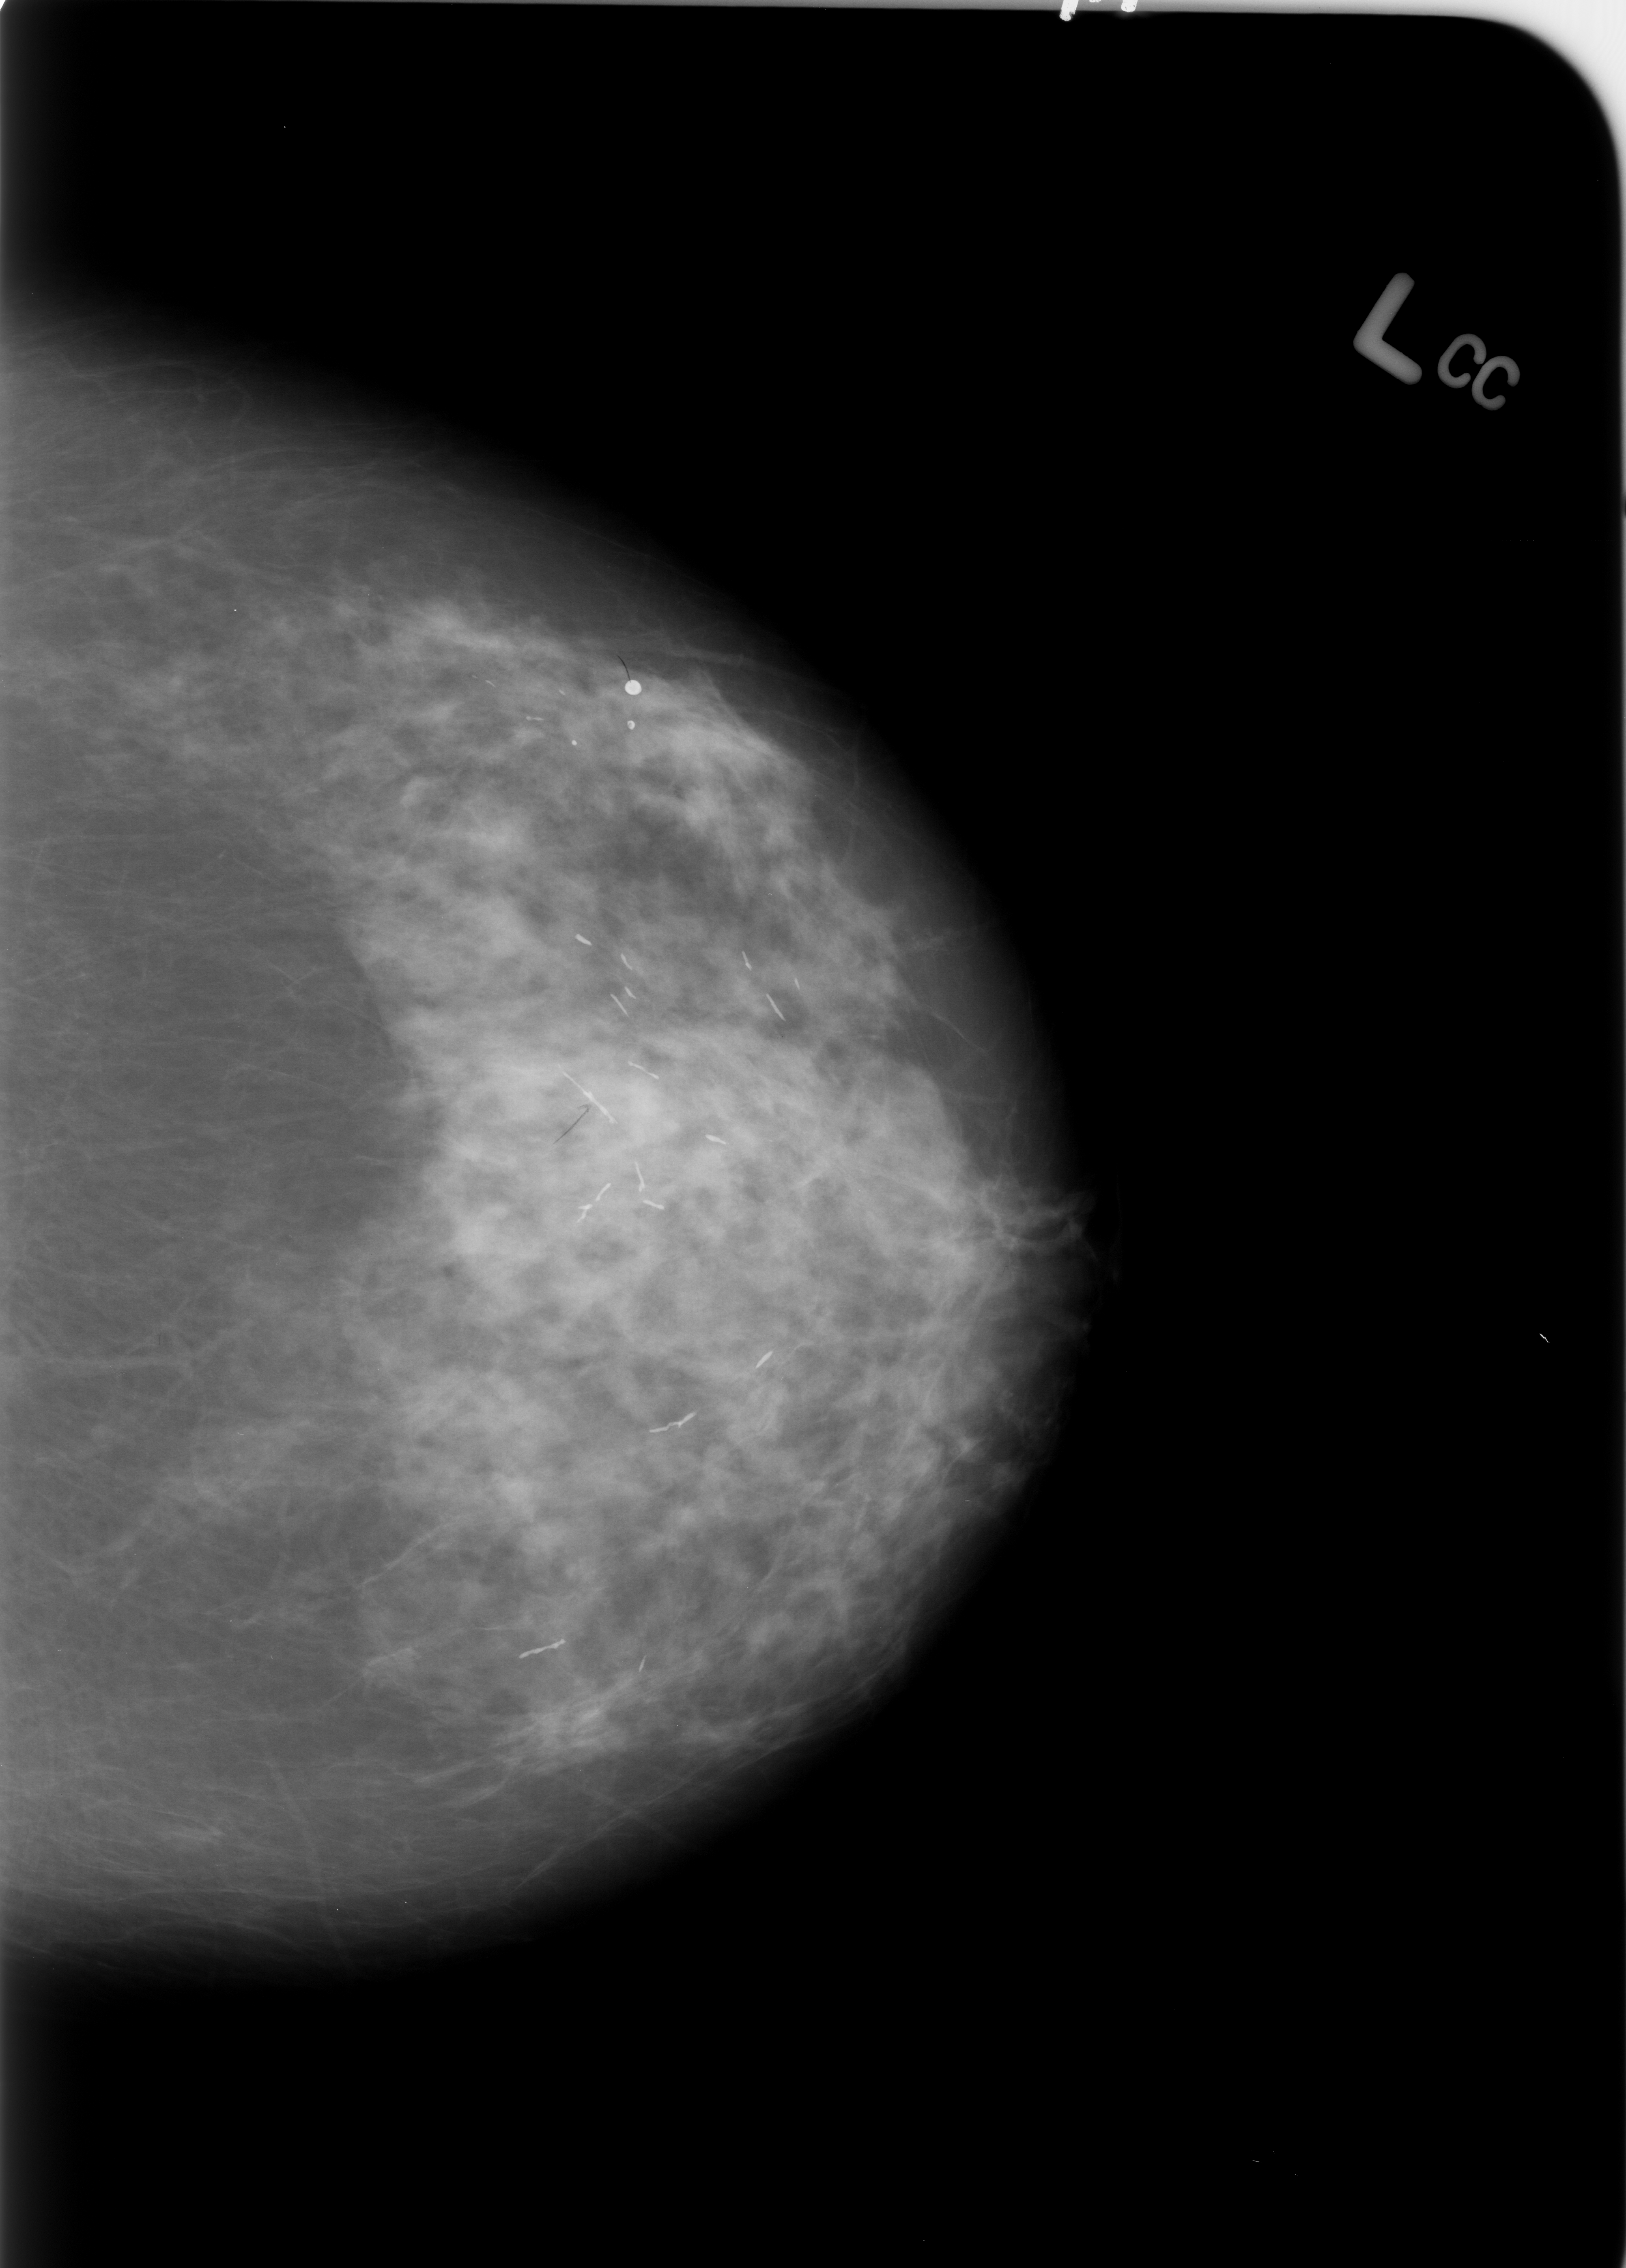
Mammogram (digitized film); left breast; CC view; breast composition: heterogeneously dense (BI-RADS density category 3 of 4); 1626 × 2268 image matrix.
Expert-marked regions of interest on this film, with their recorded descriptors:
- Finding 1 of 6: calcifications, morphology large rodlike / round and regular, distribution regional; BI-RADS assessment category 2; subtlety rating 5 on a 1 (subtle) to 5 (obvious) scale; benign; no additional work-up was recommended (outcome (as recorded, no biopsy): benign without callback): box from (x=499, y=1625) to (x=588, y=1669) px
- Finding 2 of 6: calcifications, morphology large rodlike / round and regular, distribution regional; BI-RADS assessment category 2; subtlety rating 5 on a 1 (subtle) to 5 (obvious) scale; outcome (as recorded, no biopsy): benign without callback (not worked up further): (x=561, y=1077)–(x=673, y=1221)
- Finding 3 of 6: calcifications, morphology large rodlike / round and regular, distribution regional; BI-RADS assessment category 2; subtlety rating 5 on a 1 (subtle) to 5 (obvious) scale; benign; no additional work-up was recommended (outcome (as recorded, no biopsy): benign without callback): (x=564, y=918)–(x=656, y=1036)
- Finding 4 of 6: calcifications, morphology large rodlike / round and regular, distribution regional; BI-RADS assessment category 2; benign; no additional work-up was recommended (outcome (as recorded, no biopsy): benign without callback): (x=606, y=668)–(x=663, y=741)
- Finding 5 of 6: calcifications, morphology large rodlike / round and regular, distribution regional; BI-RADS assessment category 2; outcome (as recorded, no biopsy): benign without callback (not worked up further): (x=626, y=1317)–(x=803, y=1442)
- Finding 6 of 6: calcifications, morphology large rodlike / round and regular, distribution regional; BI-RADS assessment category 2; subtlety rating 5 on a 1 (subtle) to 5 (obvious) scale; outcome (as recorded, no biopsy): benign without callback (not worked up further): (x=730, y=944)–(x=806, y=1036)